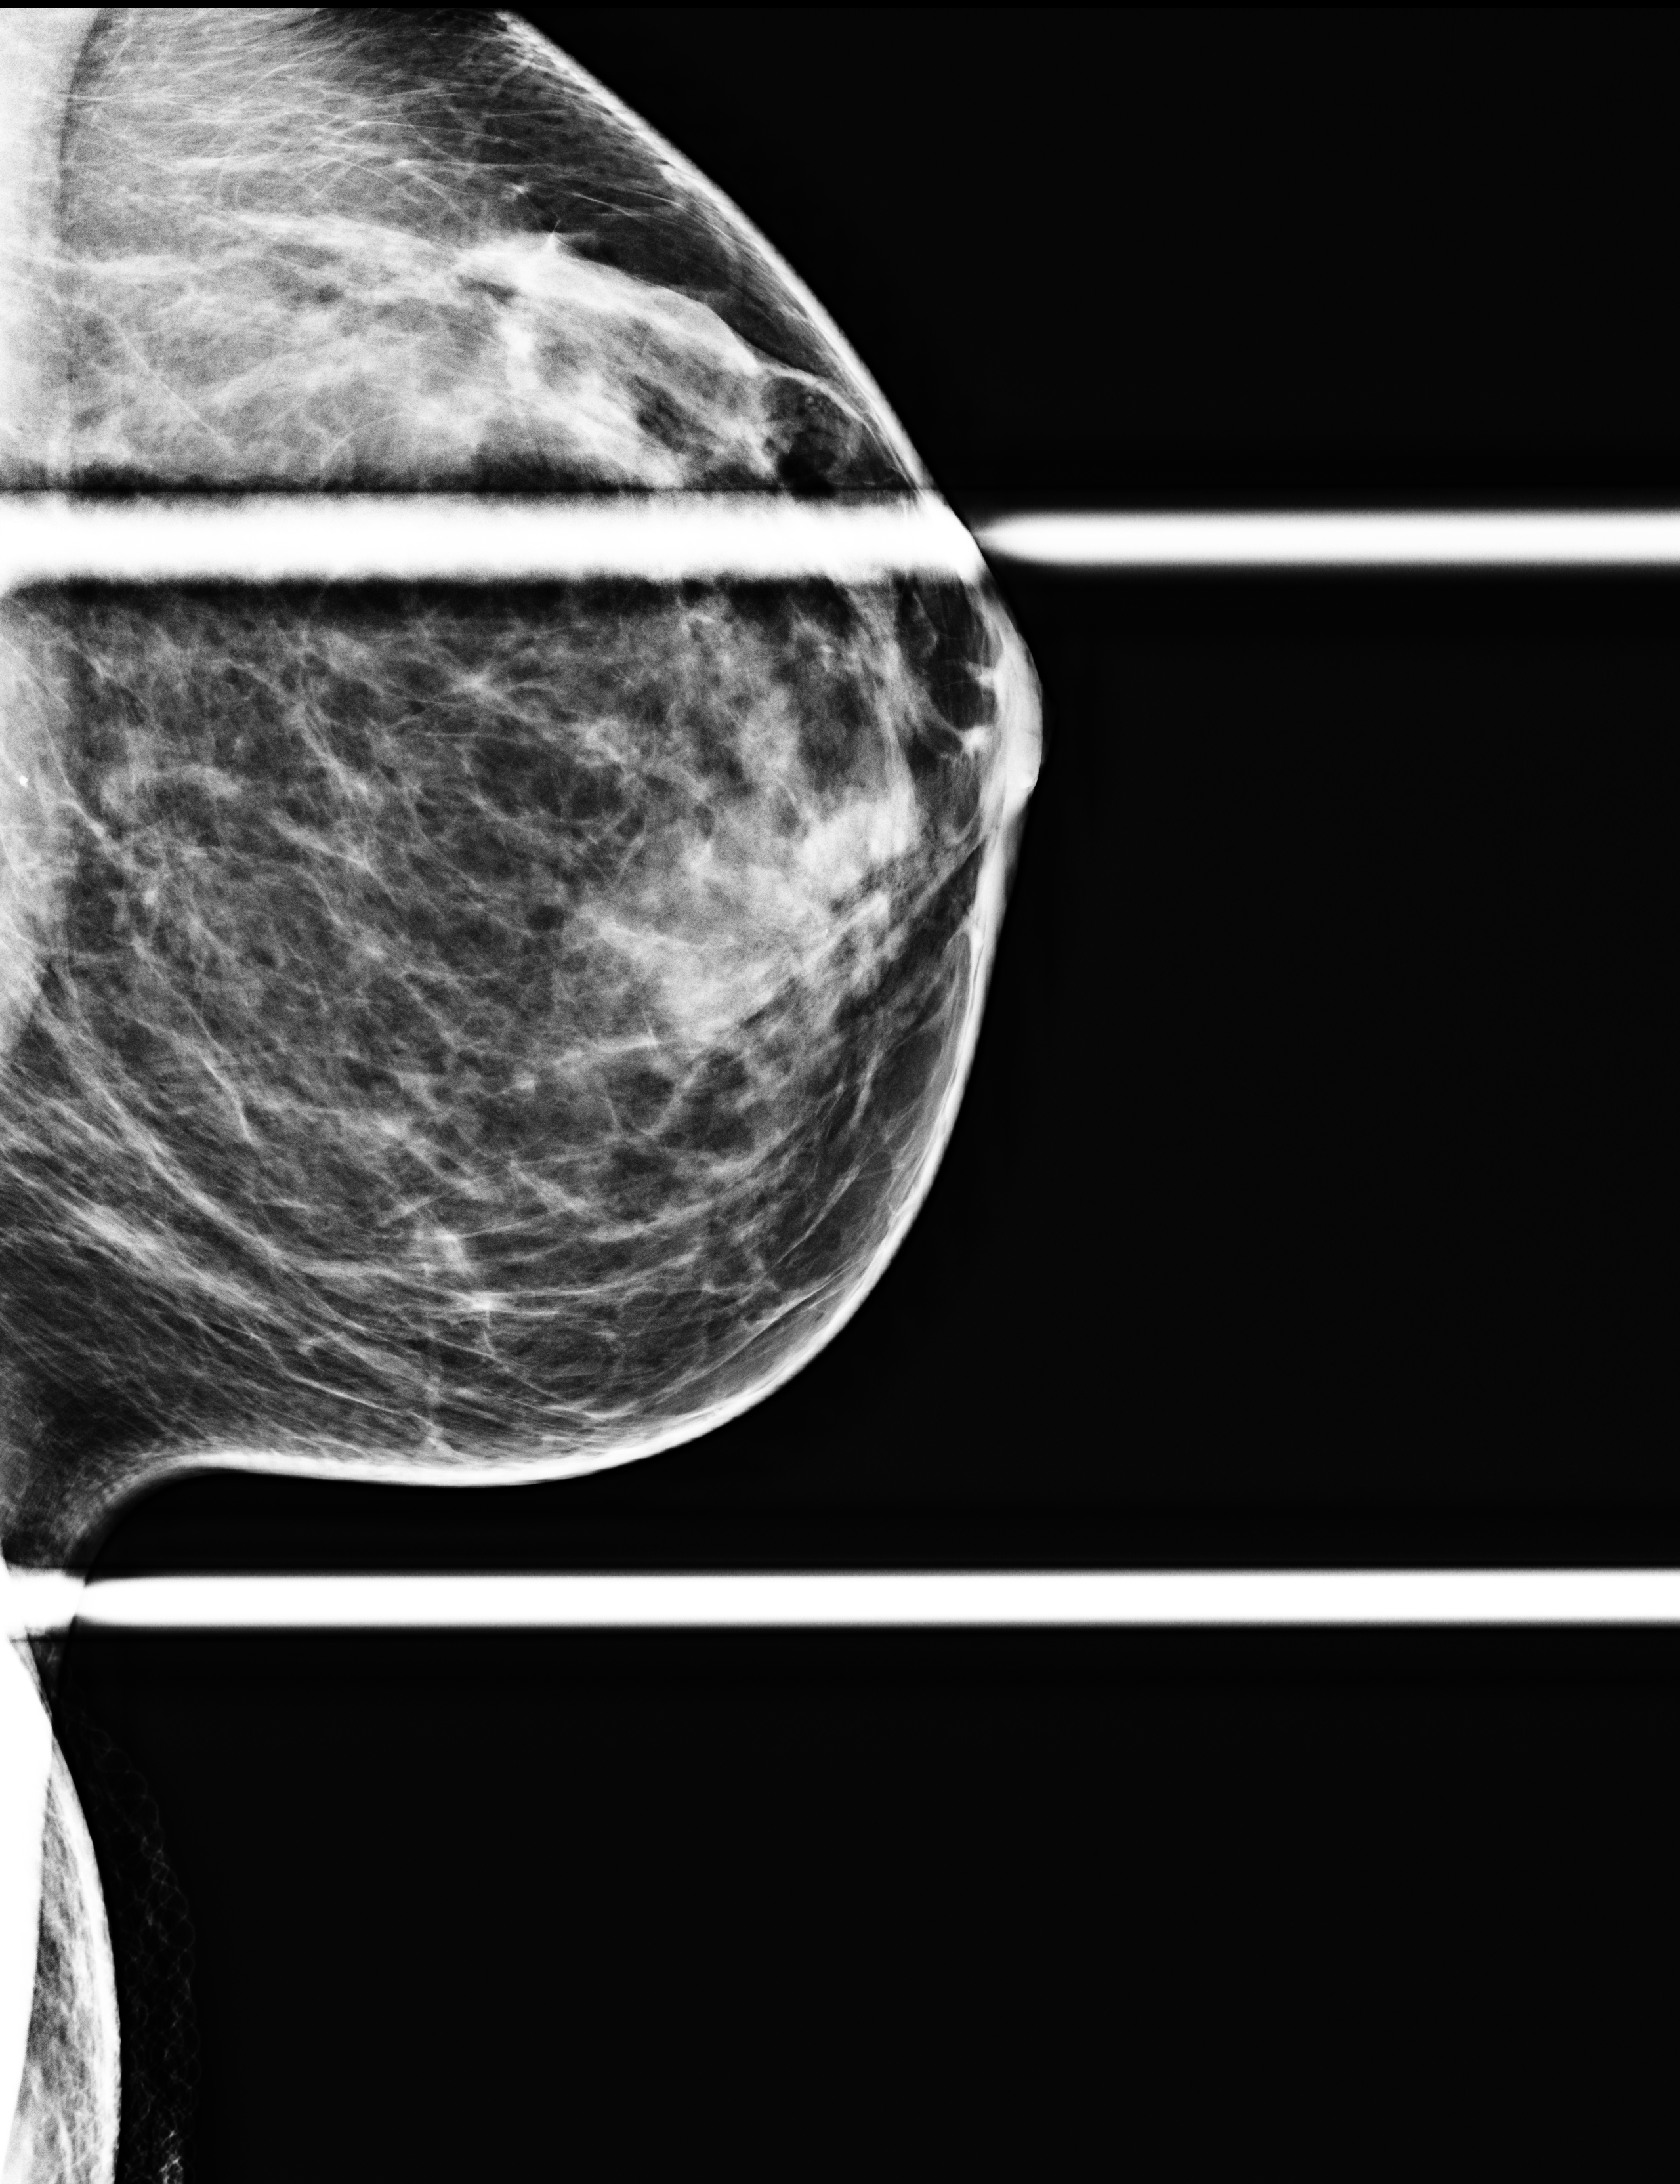
Additional work-up view, compressed breast thickness 51 mm. Patient aged 45 years (female).
Image type: full-field digital mammogram. Breast: left. Projection: mediolateral oblique (MLO) view, spot compression.